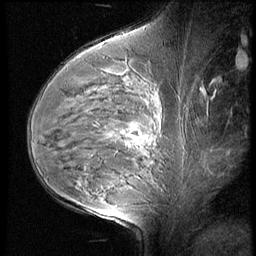
Breast MRI (dynamic contrast-enhanced), one sagittal slice; position 37 of 60 along the scan axis; 3 images stored at this slice position (order not interpretable as contrast timing); 1.5 T; TE 4.2 ms, TR 9 ms; 2.5 mm slice thickness; 256 × 256 image matrix, field of view 180 × 180 mm. Patient: female, 35 years. From the clinical record (not read from this slice): setting: breast cancer imaged before/during neoadjuvant chemotherapy; receptor status: HR-positive, HER2-negative.
Outlined on this slice (semi-automatically segmented with operator editing):
- analysis volume of interest (the breast-tissue region the enhancement analysis was run in; not a lesion): bounding box <56,58,176,202> (left, top, right, bottom; pixels)
- tumour enhancement mask (voxels above the 140 % enhancement threshold inside the analysis volume of interest): <110,134,141,144>